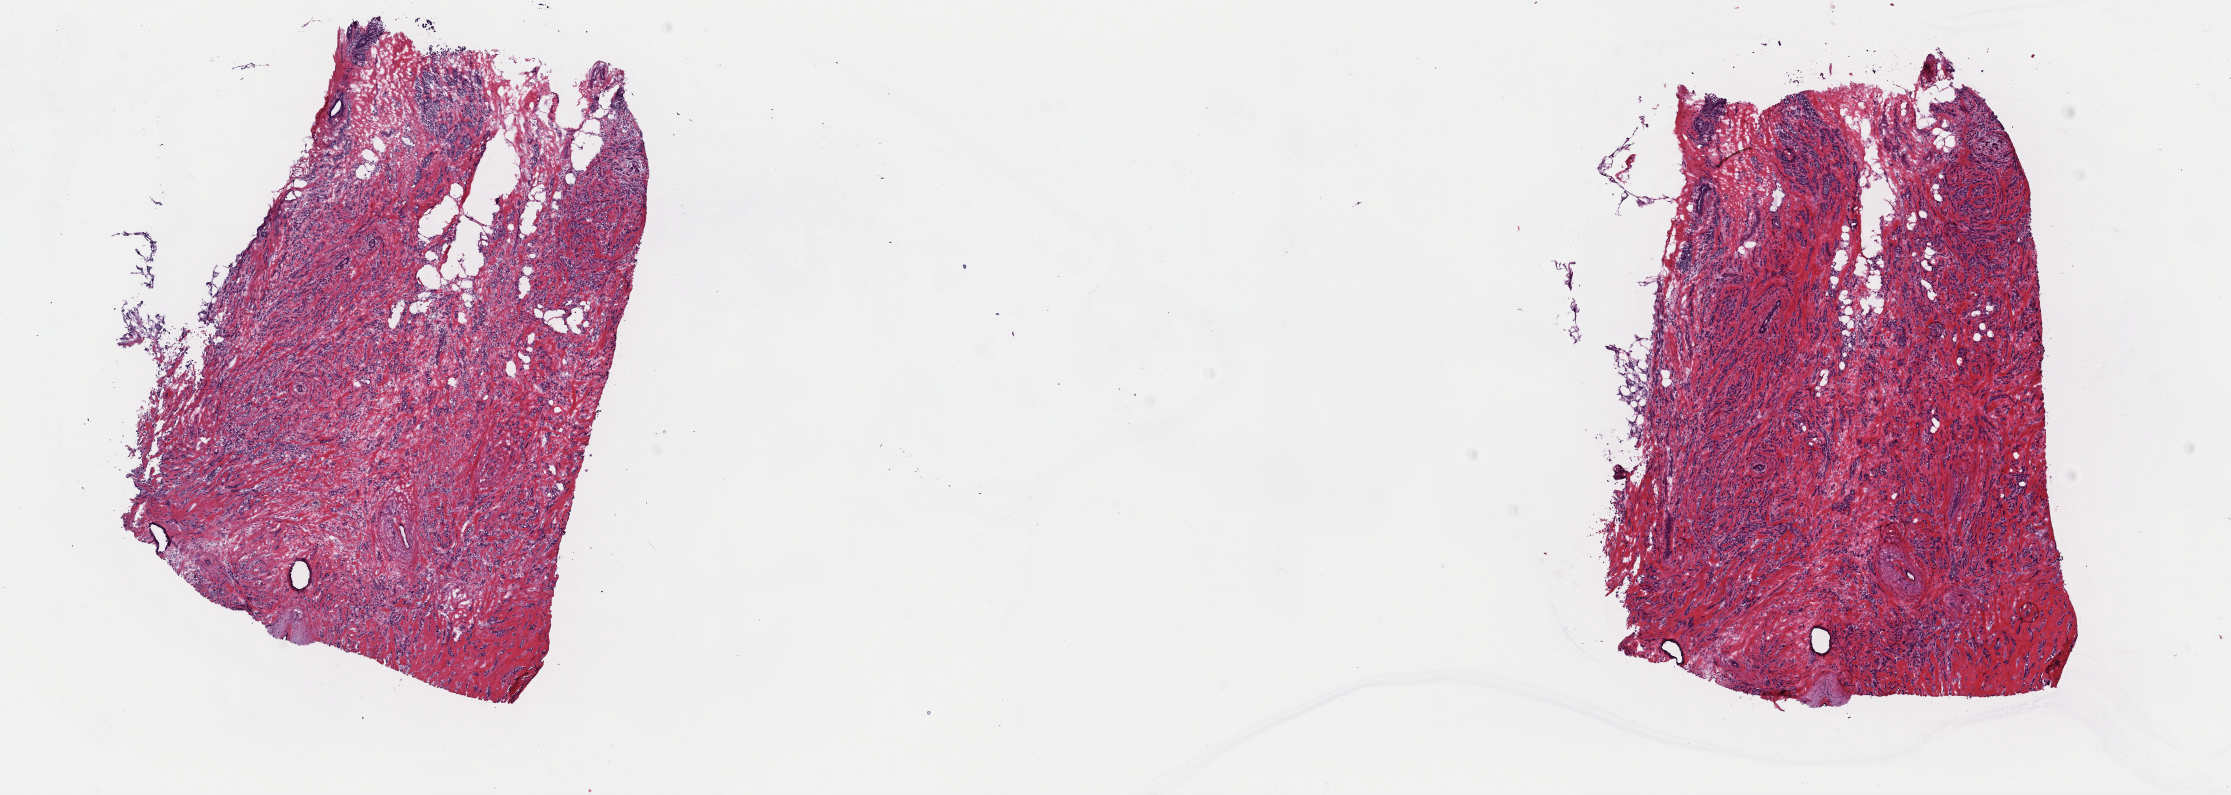
Digitized Hematoxylin and eosin (H&E) stained tissue section (whole slide) — whole scanned area (about 17.6 x 6.3 mm, slide scanned at 40x) shown as a low-resolution overview; frozen section from the top of the tissue portion; breast, primary tumour sample. Patient: female, age at initial diagnosis 66 years. Composition of this section per pathologist review: tumour cells 95%, tumour nuclei 85%, normal cells 5%, stromal cells 0%, necrosis 0%. Inflammatory infiltration, as recorded: lymphocyte infiltration 0%, monocyte infiltration 0%, neutrophil infiltration 0%.
AJCC pathologic stage: IIB. Pathologic diagnosis: Lobular carcinoma, NOS.